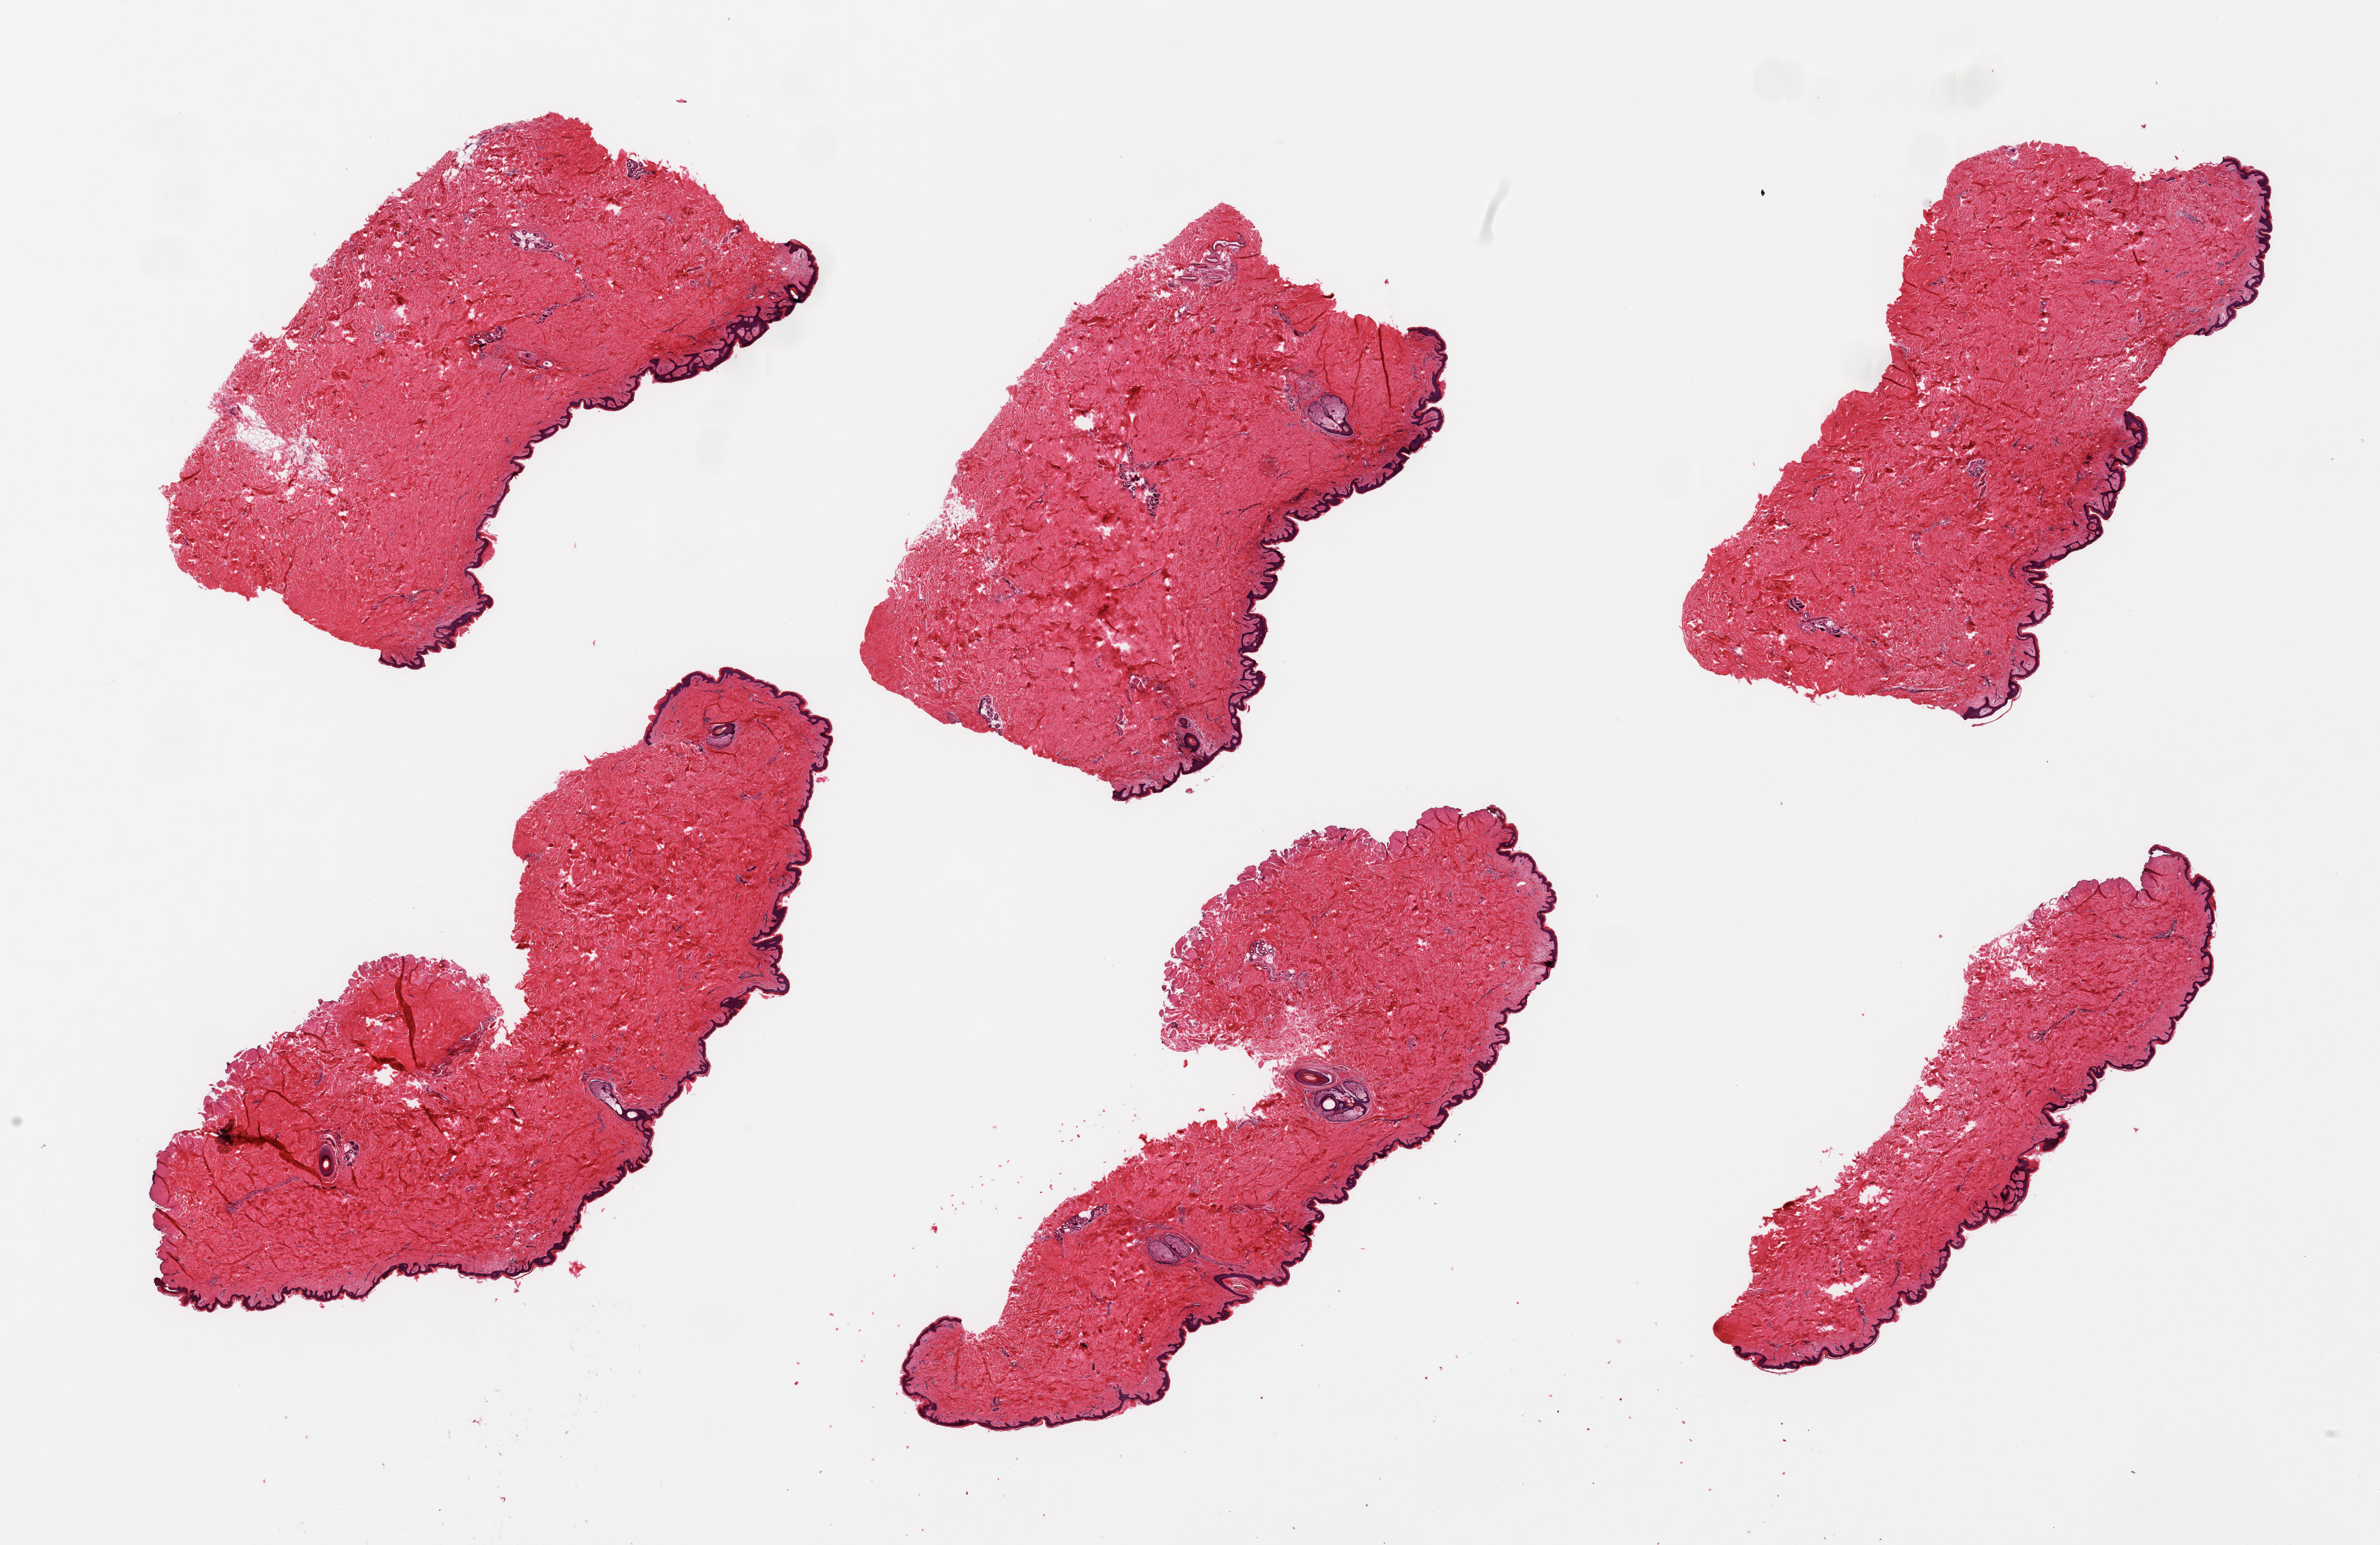
Digitized hematoxylin and eosin (H&E)-stained section — whole scanned area (about 27.6 x 17.9 mm, slide scanned at 20x) shown as a low-resolution overview, PAXgene-fixed paraffin-embedded (PFPE) section, sampled site (target tissue): skin of suprapubic region, tissue donor sample. Donor: male.
* review note (as recorded): 6 pieces; 5% dermal fat; well trimmed